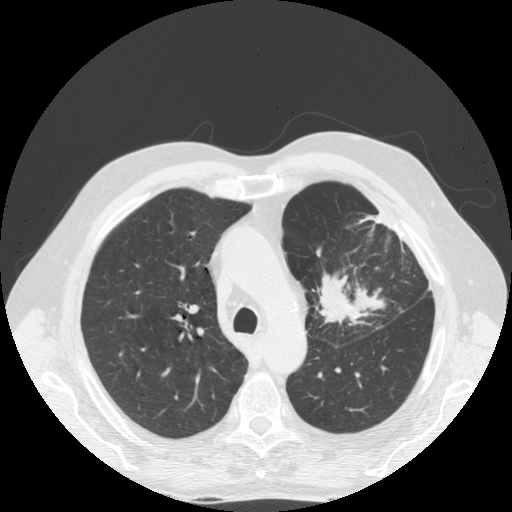
Low-dose screening chest CT, axial slice, first (baseline) screen, lung window (W 1500 / L -600 HU), 2.5 mm slice thickness. Male participant, aged 70 years at enrolment. Former smoker at enrolment.
- Lesion marked by an expert reader, bounding box <295,255,395,344> (left, top, right, bottom; pixels).
- Screening reader's record for this exam (one nodule recorded; not confirmed to be the boxed lesion): non-calcified nodule or mass ≥4 mm, left upper lobe, 46 × 31 mm, spiculated (stellate) margins, soft tissue attenuation.
- Later outcome: lung cancer diagnosed 78 days after this screen — squamous cell carcinoma, NOS, left upper lobe, poorly differentiated (G3), stage IIIB (AJCC 6th edition), 46 mm at pathology.